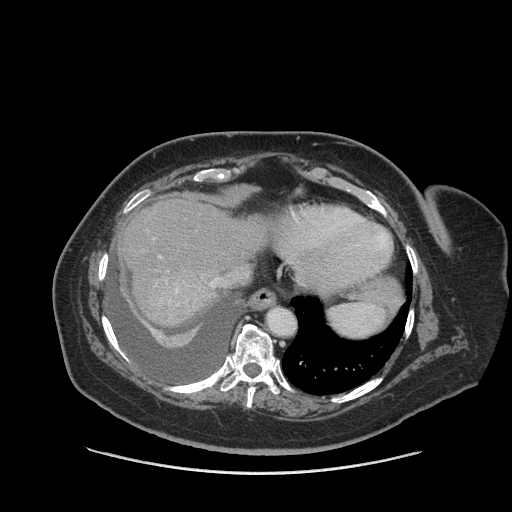
Contrast-enhanced abdominal CT (liver protocol), one axial slice. Position 73 of 91 along the scan axis. Reconstruction kernel STANDARD. Soft-tissue window (W 400 / L 40 HU). 512 × 512 image matrix. Case-level facts recorded for this patient, not image findings: diagnosis: hepatocellular carcinoma (patient treated with transarterial chemoembolisation; whether this scan precedes or follows treatment is not stated here); TNM stage (as recorded): Stage-I; Child-Pugh class: A; tumour differentiation: well differentiated.
Structures marked on this image (semi-automatic segmentation, software-assisted and operator-edited):
- abdominal aorta: bounding box [x1, y1, x2, y2] px = [268, 308, 296, 336]
- liver parenchyma outside the tumour (the mass and vessels are separate outlines, so this box may not span the whole liver): [120, 196, 266, 326]
- liver vessels: [176, 282, 214, 293]